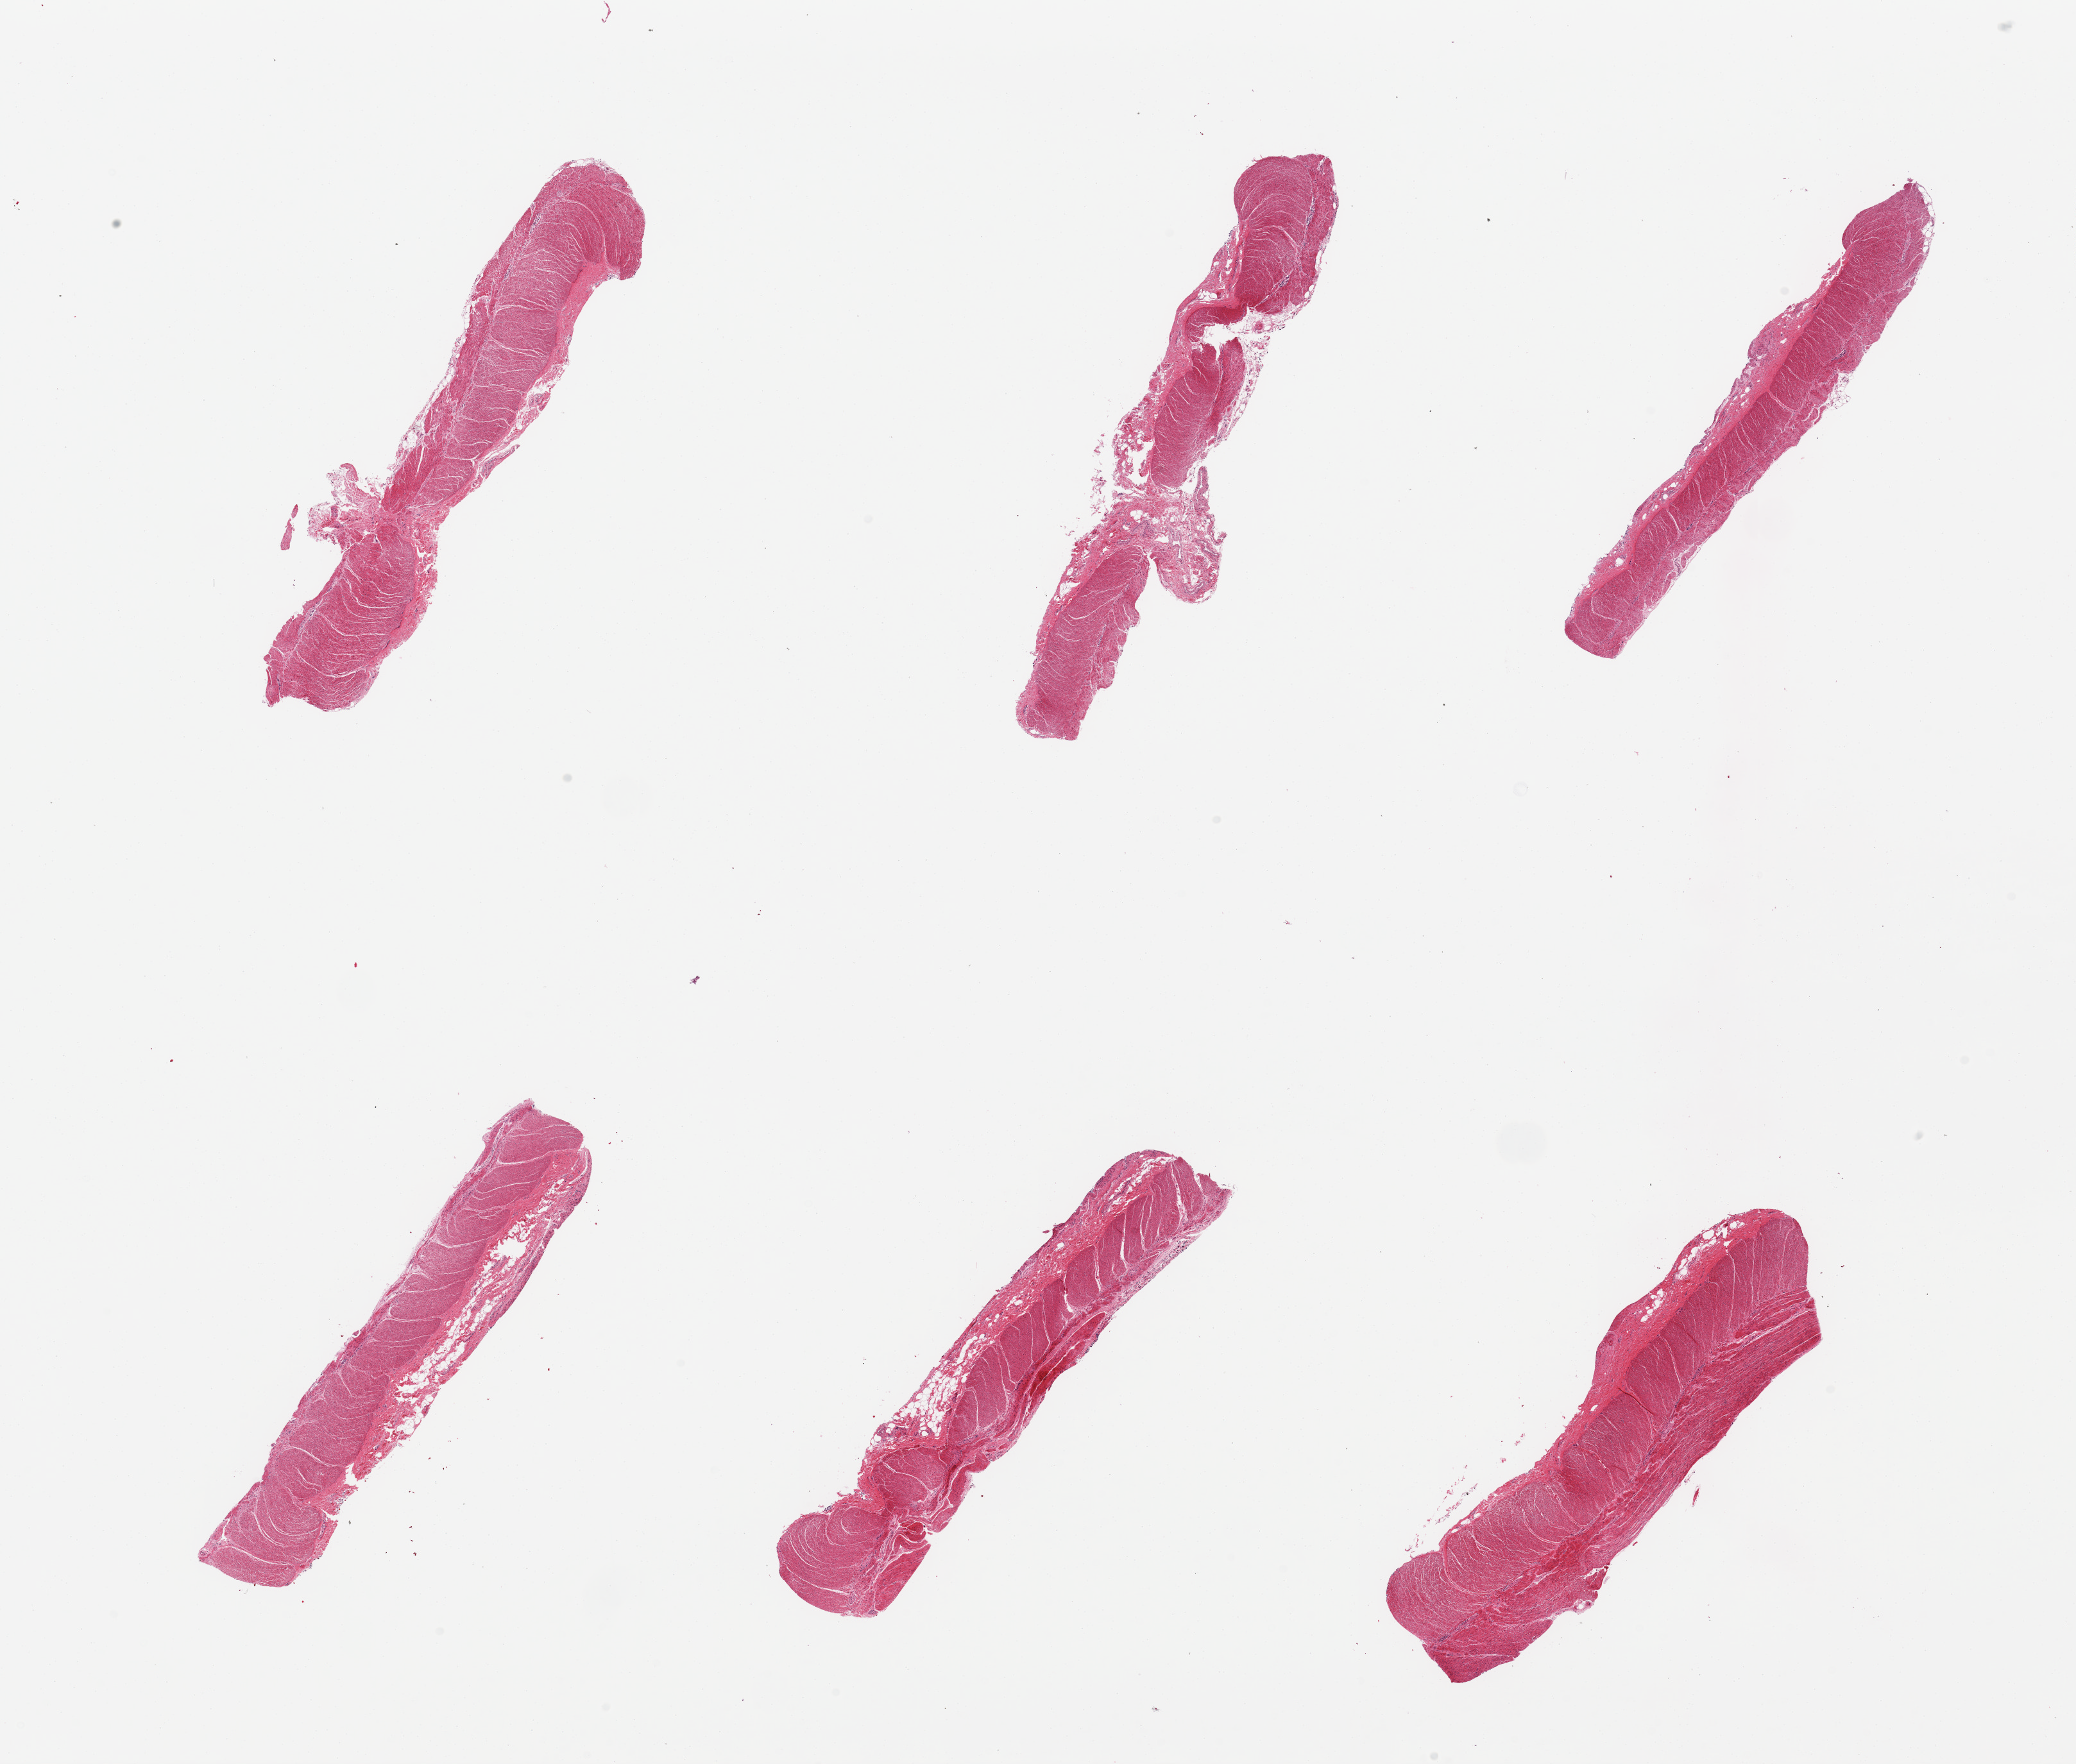
Whole-slide image, H&E stain, brightfield, a low-resolution overview of the entire scanned area, about 25.6 x 21.8 mm (slide scanned at 20x), PAXgene-fixed, paraffin-embedded tissue, target tissue: sigmoid colon, donor tissue sample.
* reviewer comment on this tissue sample: 6 pieces; well dissected muscularis with up to 20% submucosal fibrofatty tissue